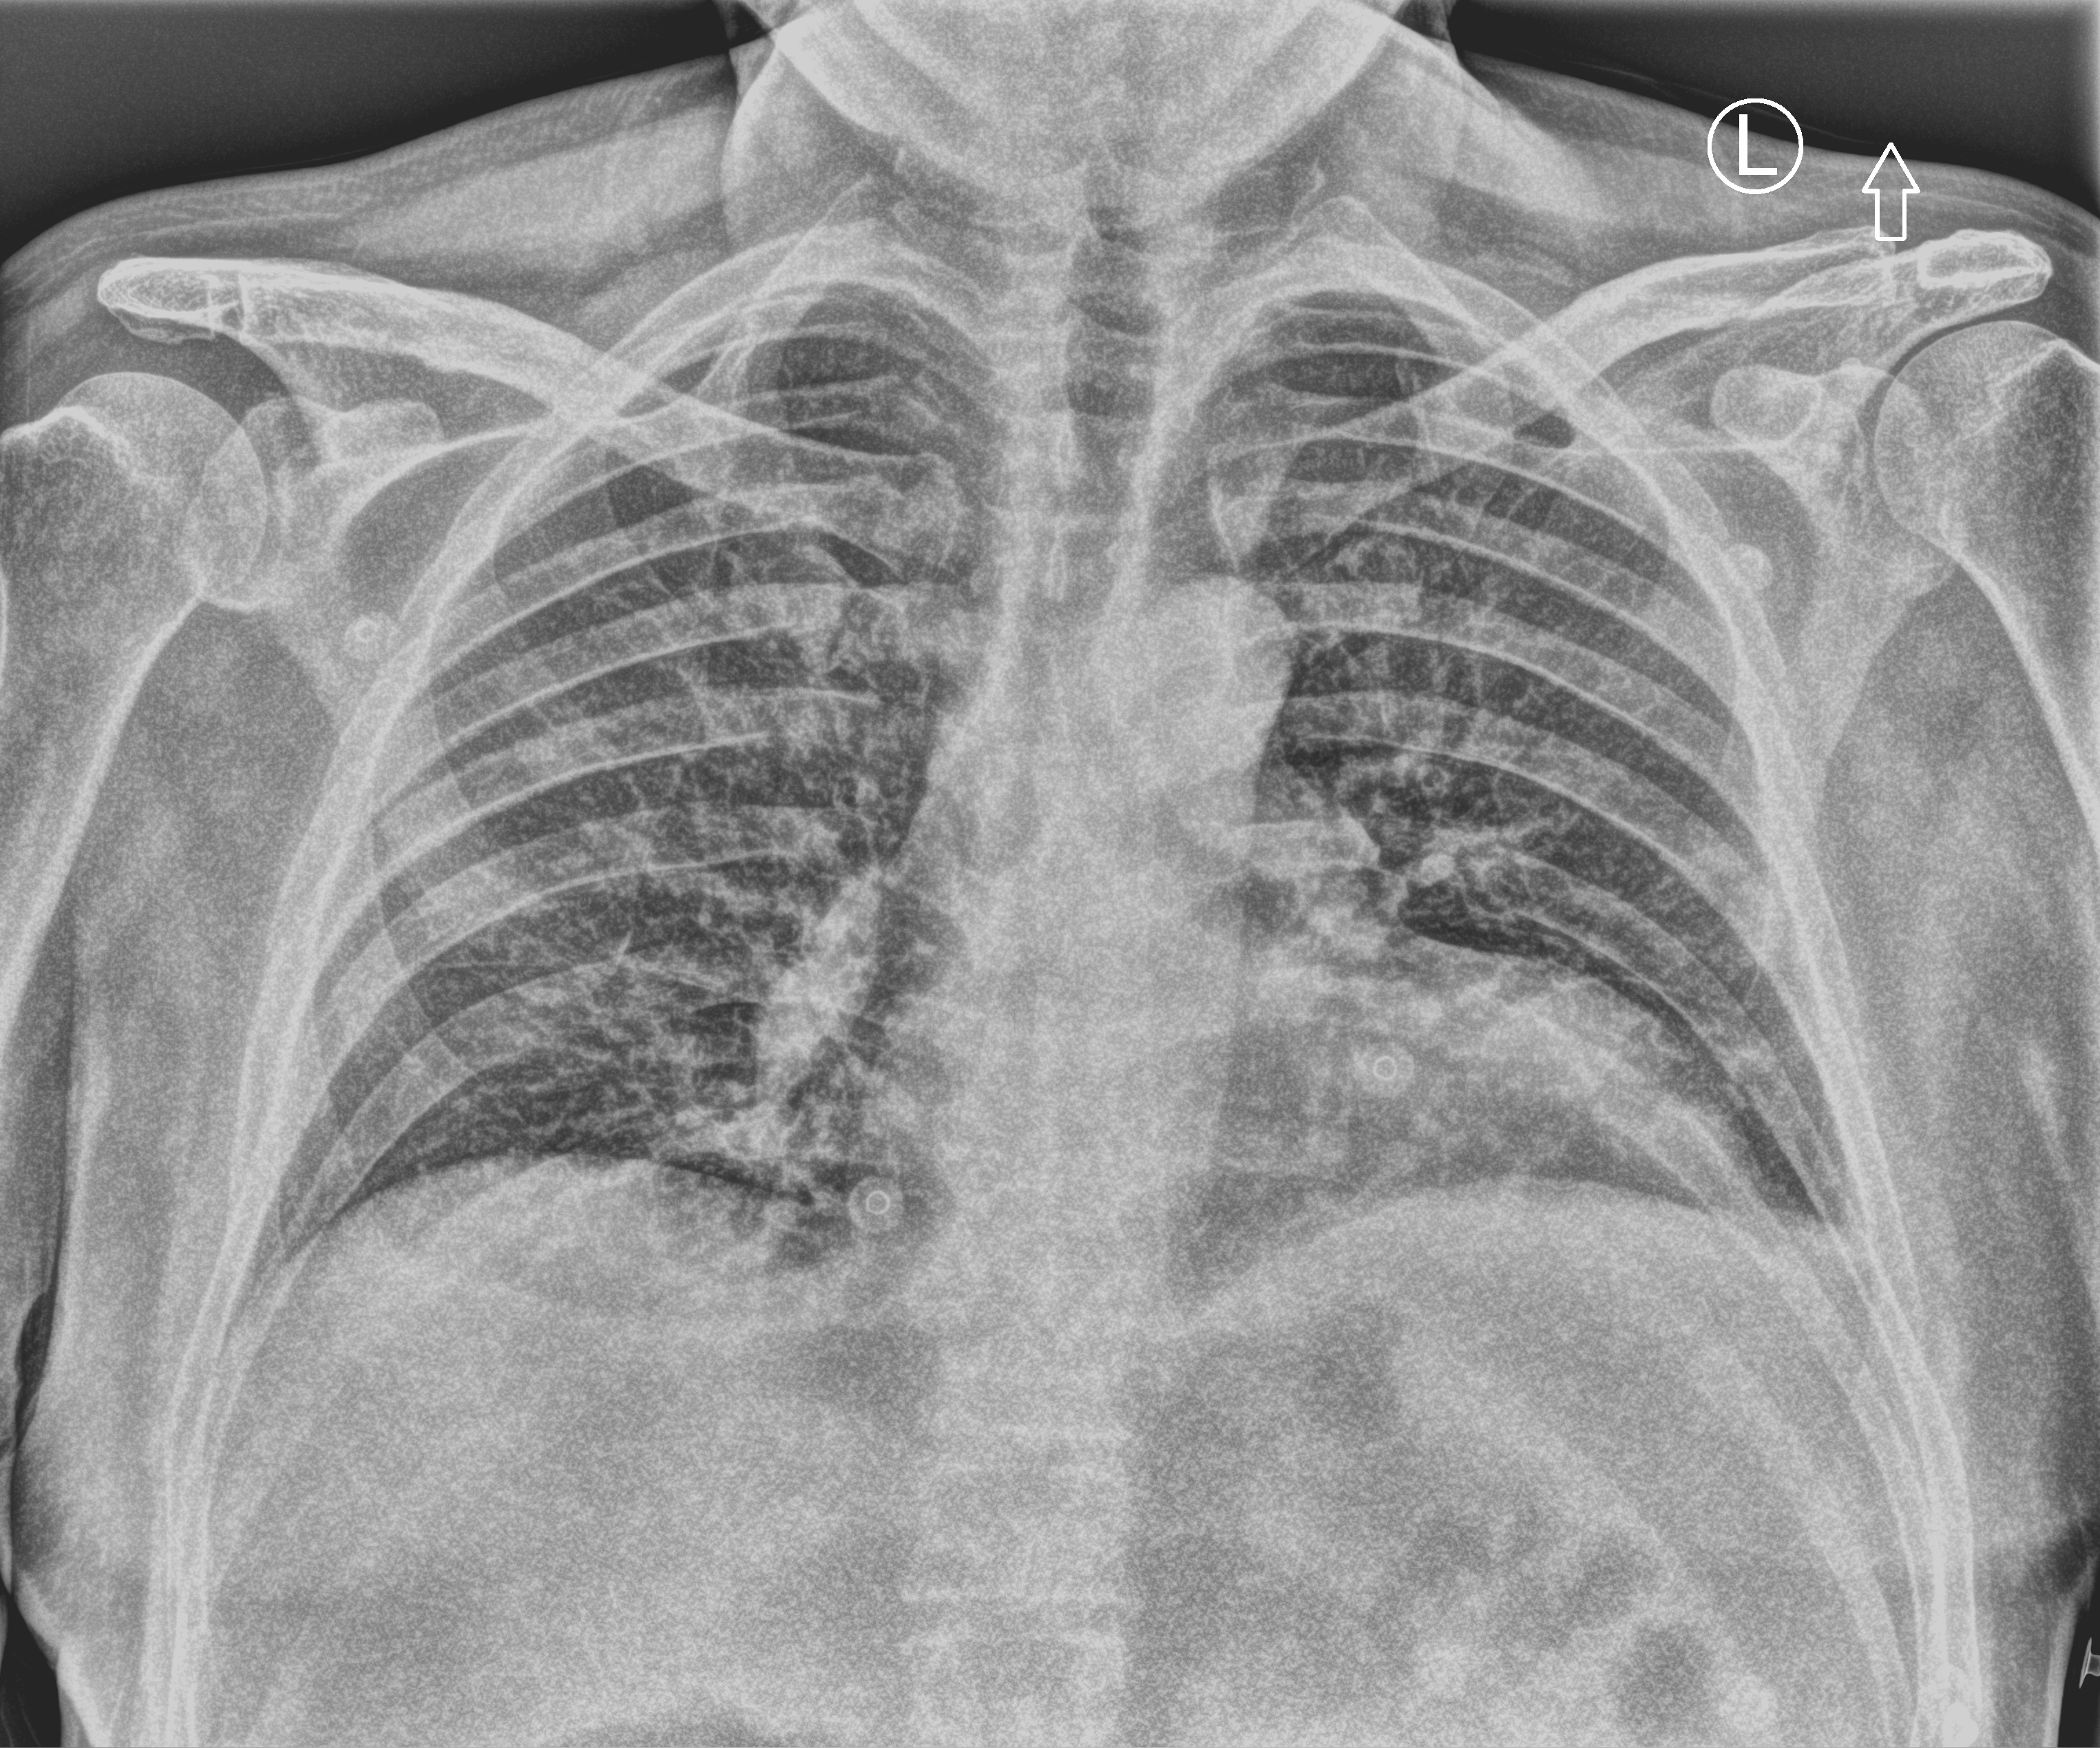
Portable chest radiograph; anteroposterior (AP) projection. Patient hospitalised with COVID-19; male, aged 60–74 years.
From the hospital-stay record, not from the radiograph (when in the stay this image was taken is not recorded):
- length of hospital stay: 24 days